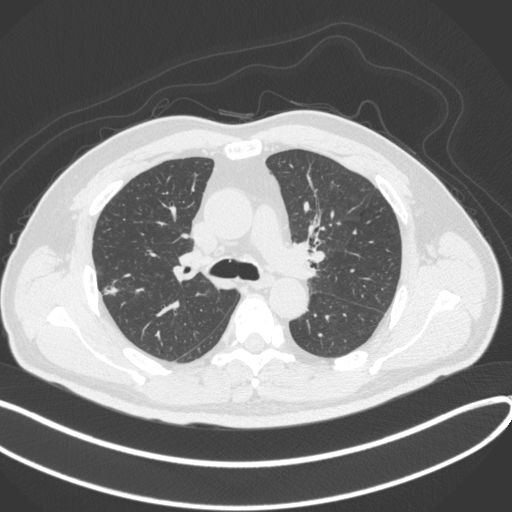
Chest CT, one axial slice; position 224 of 373 along the scan axis; reconstruction kernel B31f; lung window (W 1500 / L -600 HU); 1 mm slice thickness; 512 × 512 image matrix, field of view 400 × 400 mm. Patient: male, 60 years. Case-level facts recorded for this patient, not image findings: clinical TNM (as recorded): T1c N0 M0.
Outlined on this slice (rectangle marked by the reading radiologist):
- lung tumour (recorded histology: adenocarcinoma): bounding box <98,278,123,302> (left, top, right, bottom; pixels)